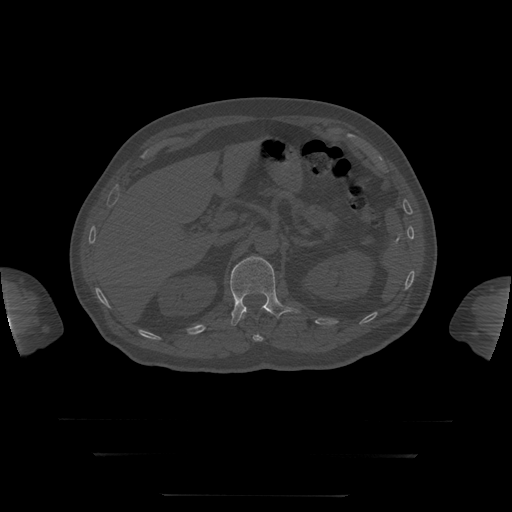
CT including the spine, one axial slice; position 56 of 397 along the scan axis; 120 kVp; bone window (W 1800 / L 400 HU); 1.25 mm slice thickness; 512 × 512 image matrix. Patient age 73 years. From the clinical record (not read from this slice): primary cancer: prostate.
Structures marked on this image (semi-automatically segmented with operator editing):
- L1 vertebra: bounding box [x1, y1, x2, y2] px = [230, 256, 299, 326]
- T12 vertebra: [242, 315, 264, 342]
- T8 vertebra: [241, 298, 272, 315]